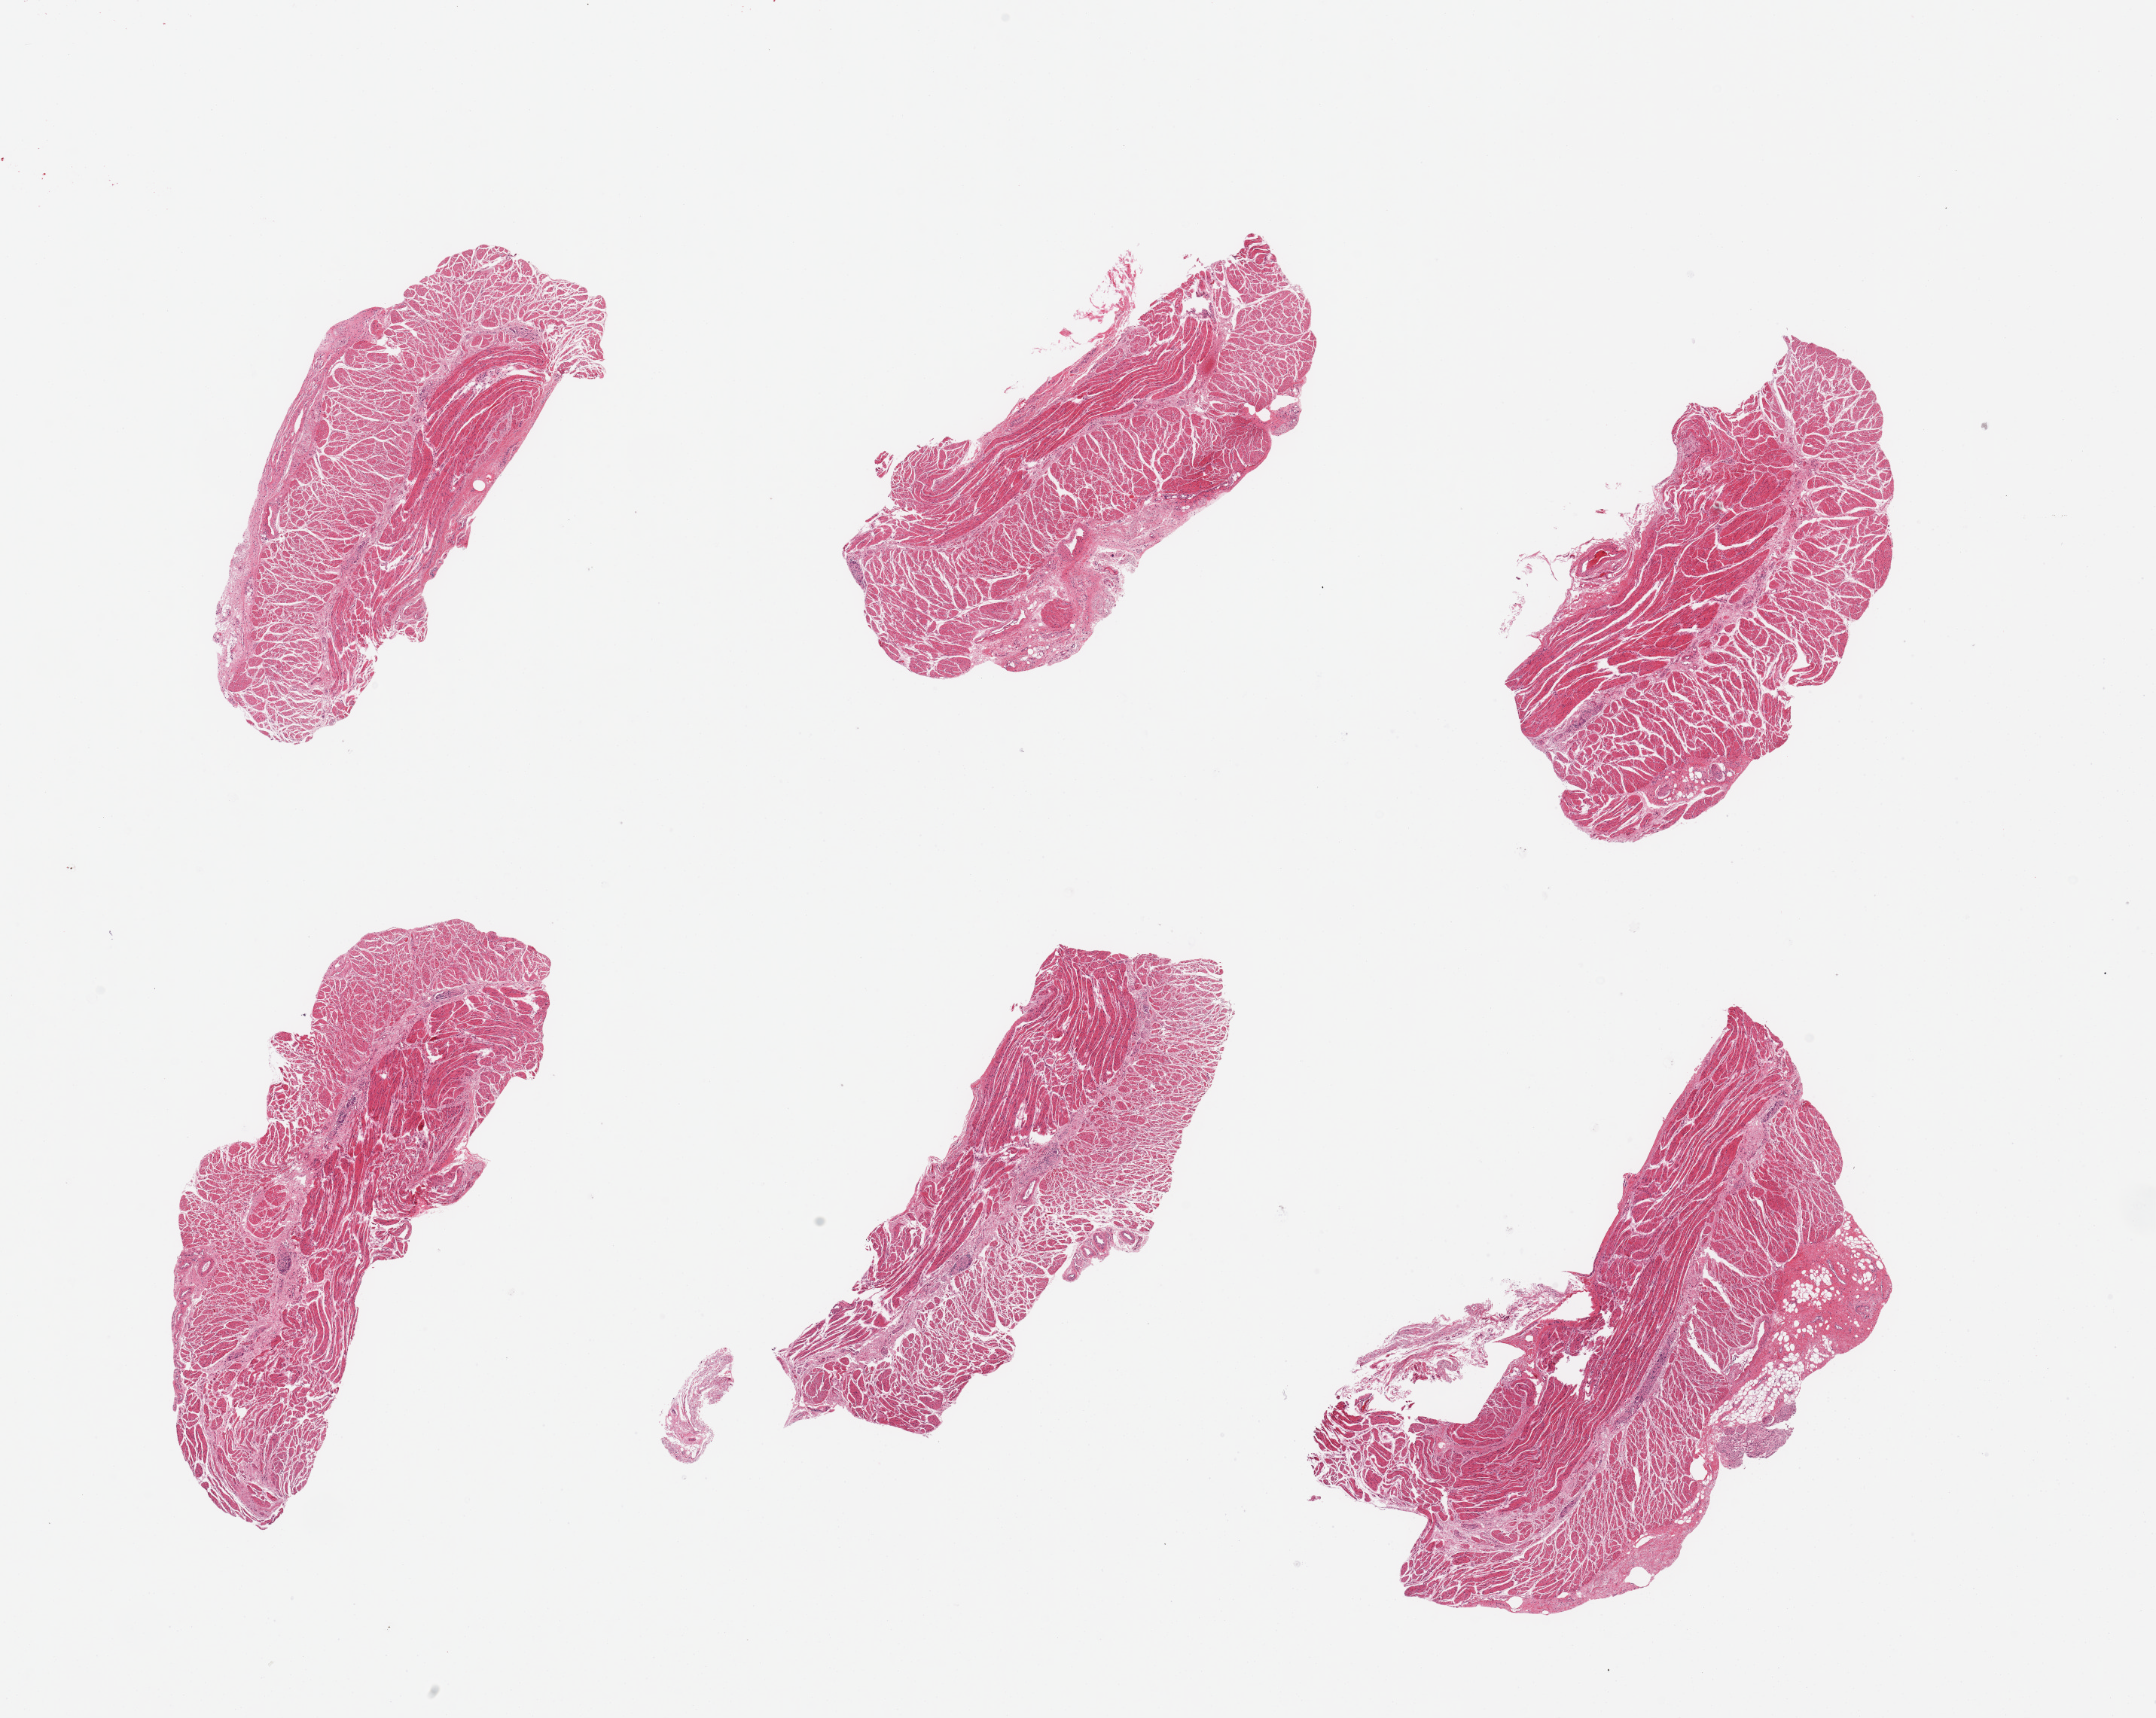
Digitized hematoxylin and eosin (H&E)-stained section, whole scanned area (about 22.6 x 18.0 mm) shown as a low-resolution overview. PAXgene-fixed, paraffin-embedded tissue. Sampled site (target tissue): gastroesophageal junction. Tissue donor sample. Donor: male.
Review note (as recorded): 6 pieces; well dissected muscularis.